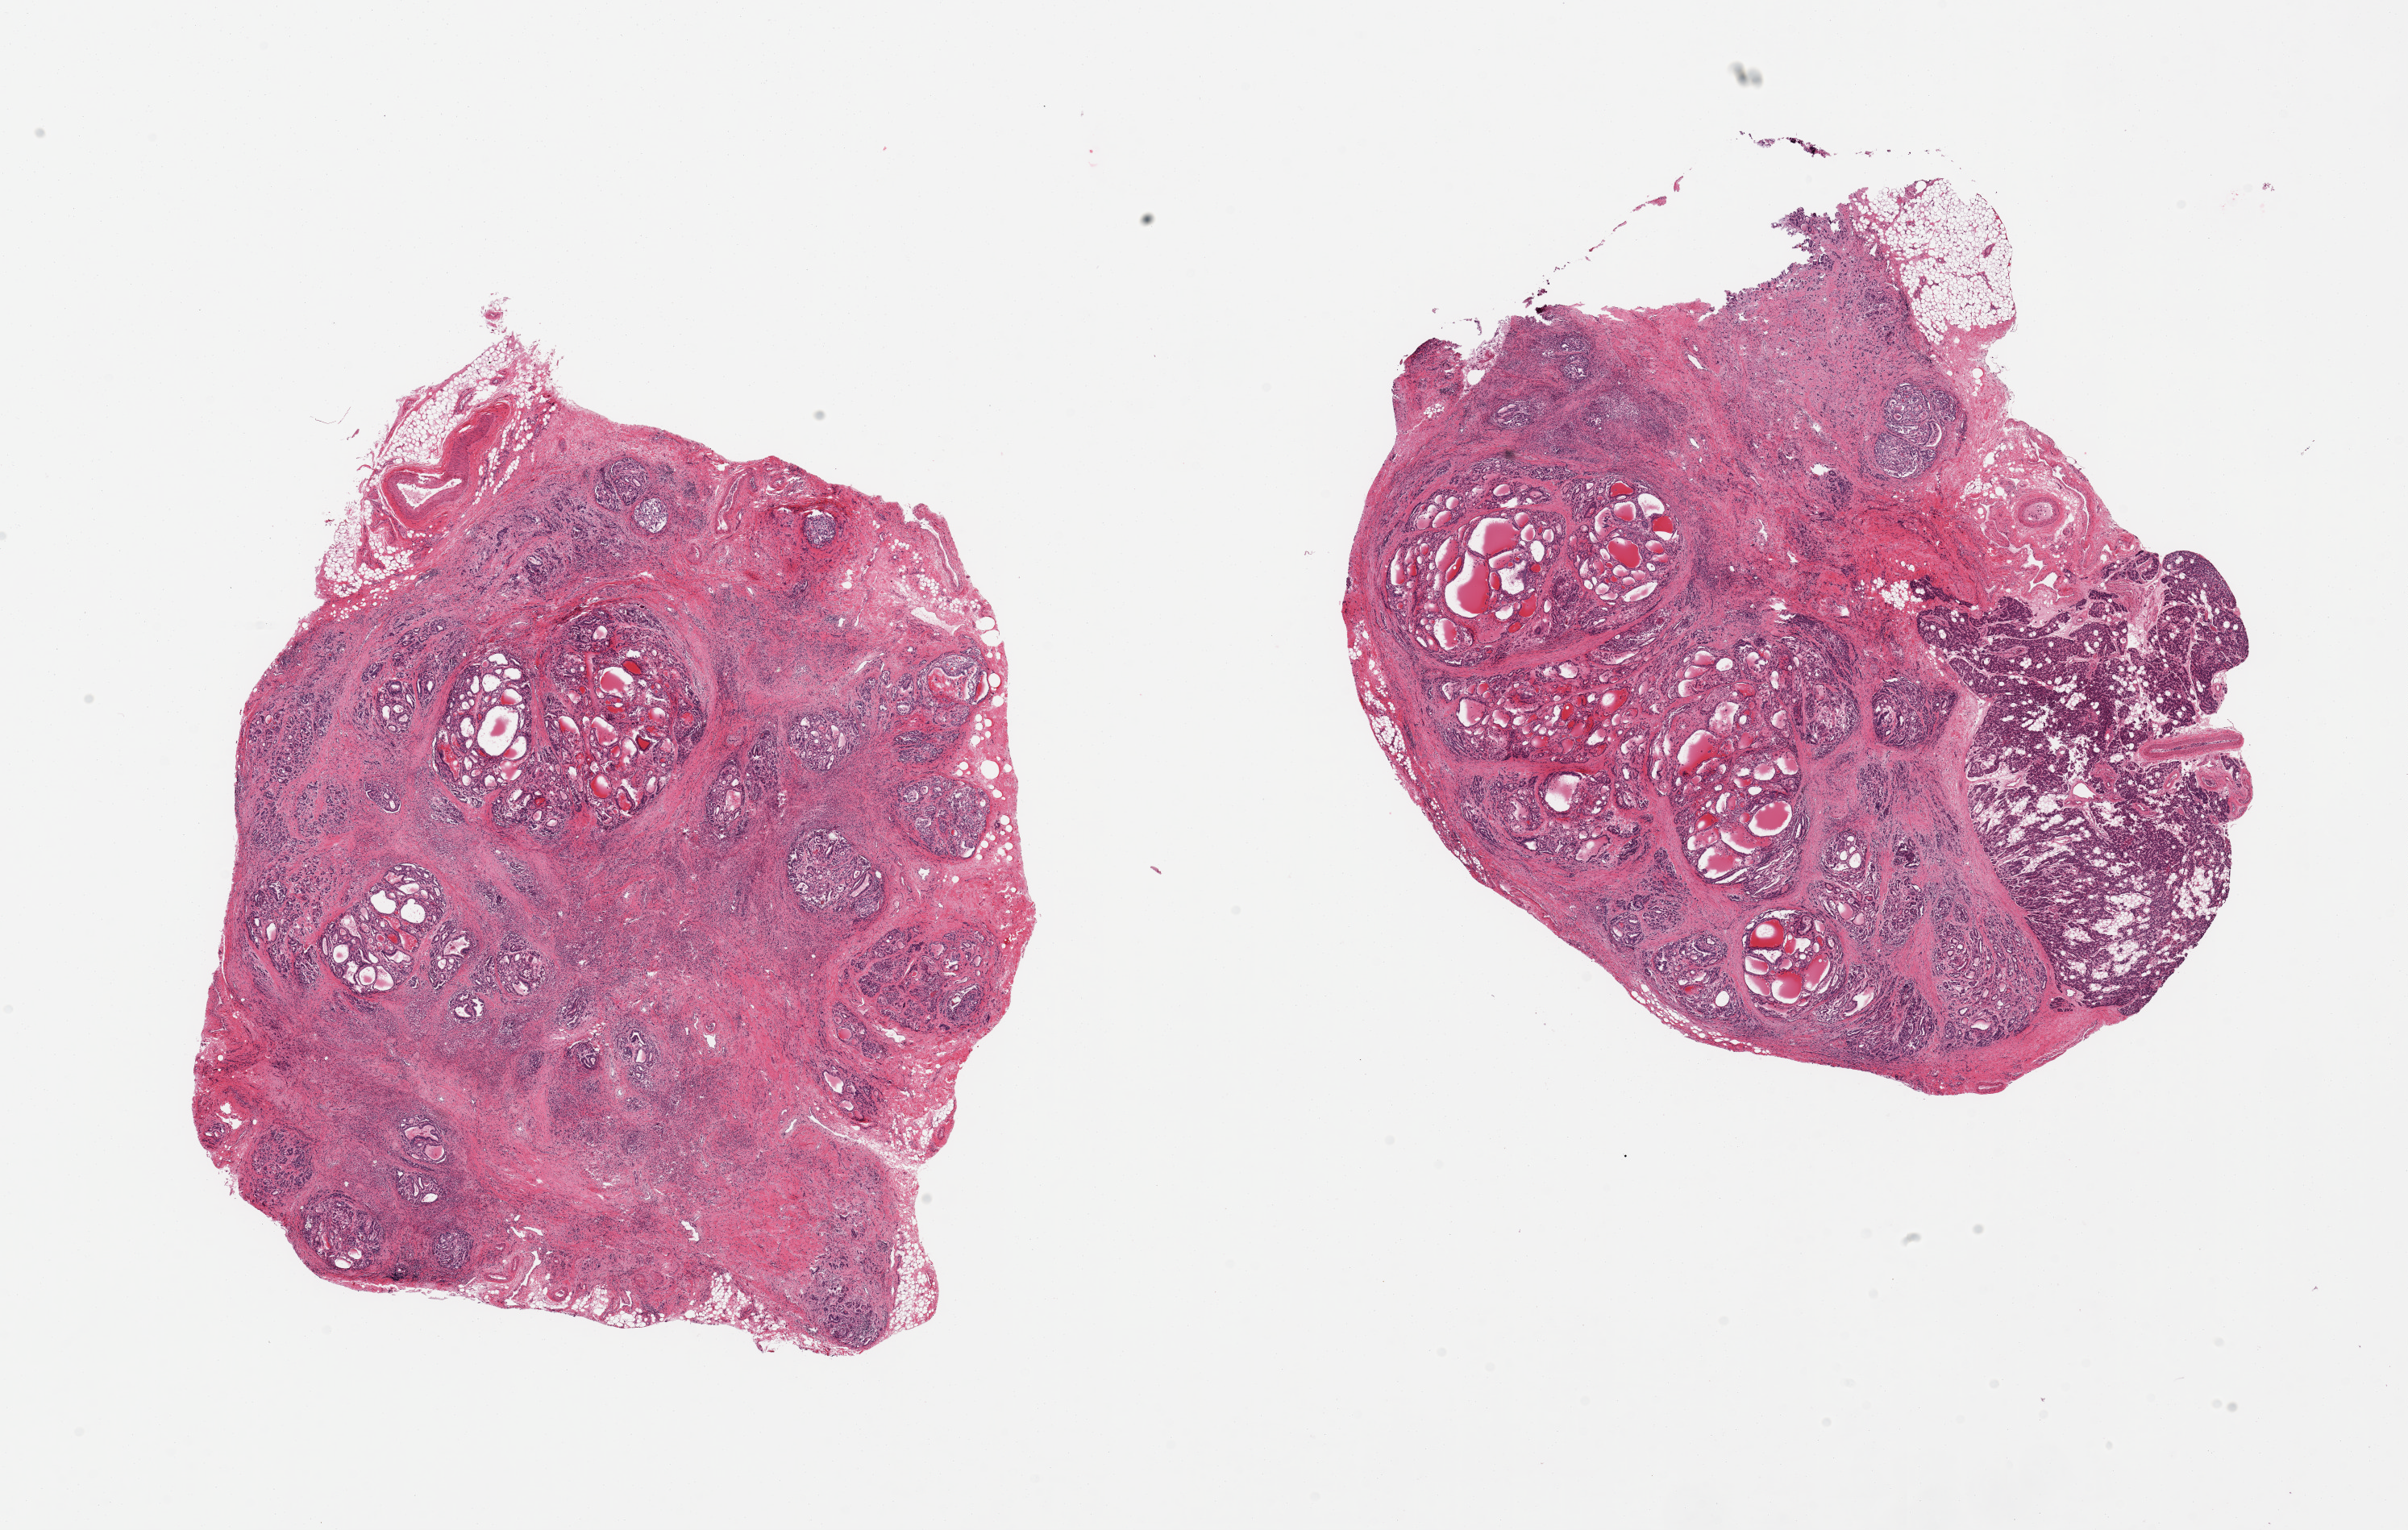
Digitized H&E-stained section, brightfield — a low-resolution overview of the entire scanned area, about 23.6 x 15.0 mm, PAXgene-fixed, paraffin-embedded tissue, section of thyroid (target tissue), donor tissue sample. Donor sex: female.
Review note (as recorded): 2 pieces, late stage goitre/thyroid itis with regressive changes; 4x3mm incidental adherent parathyroid gland.